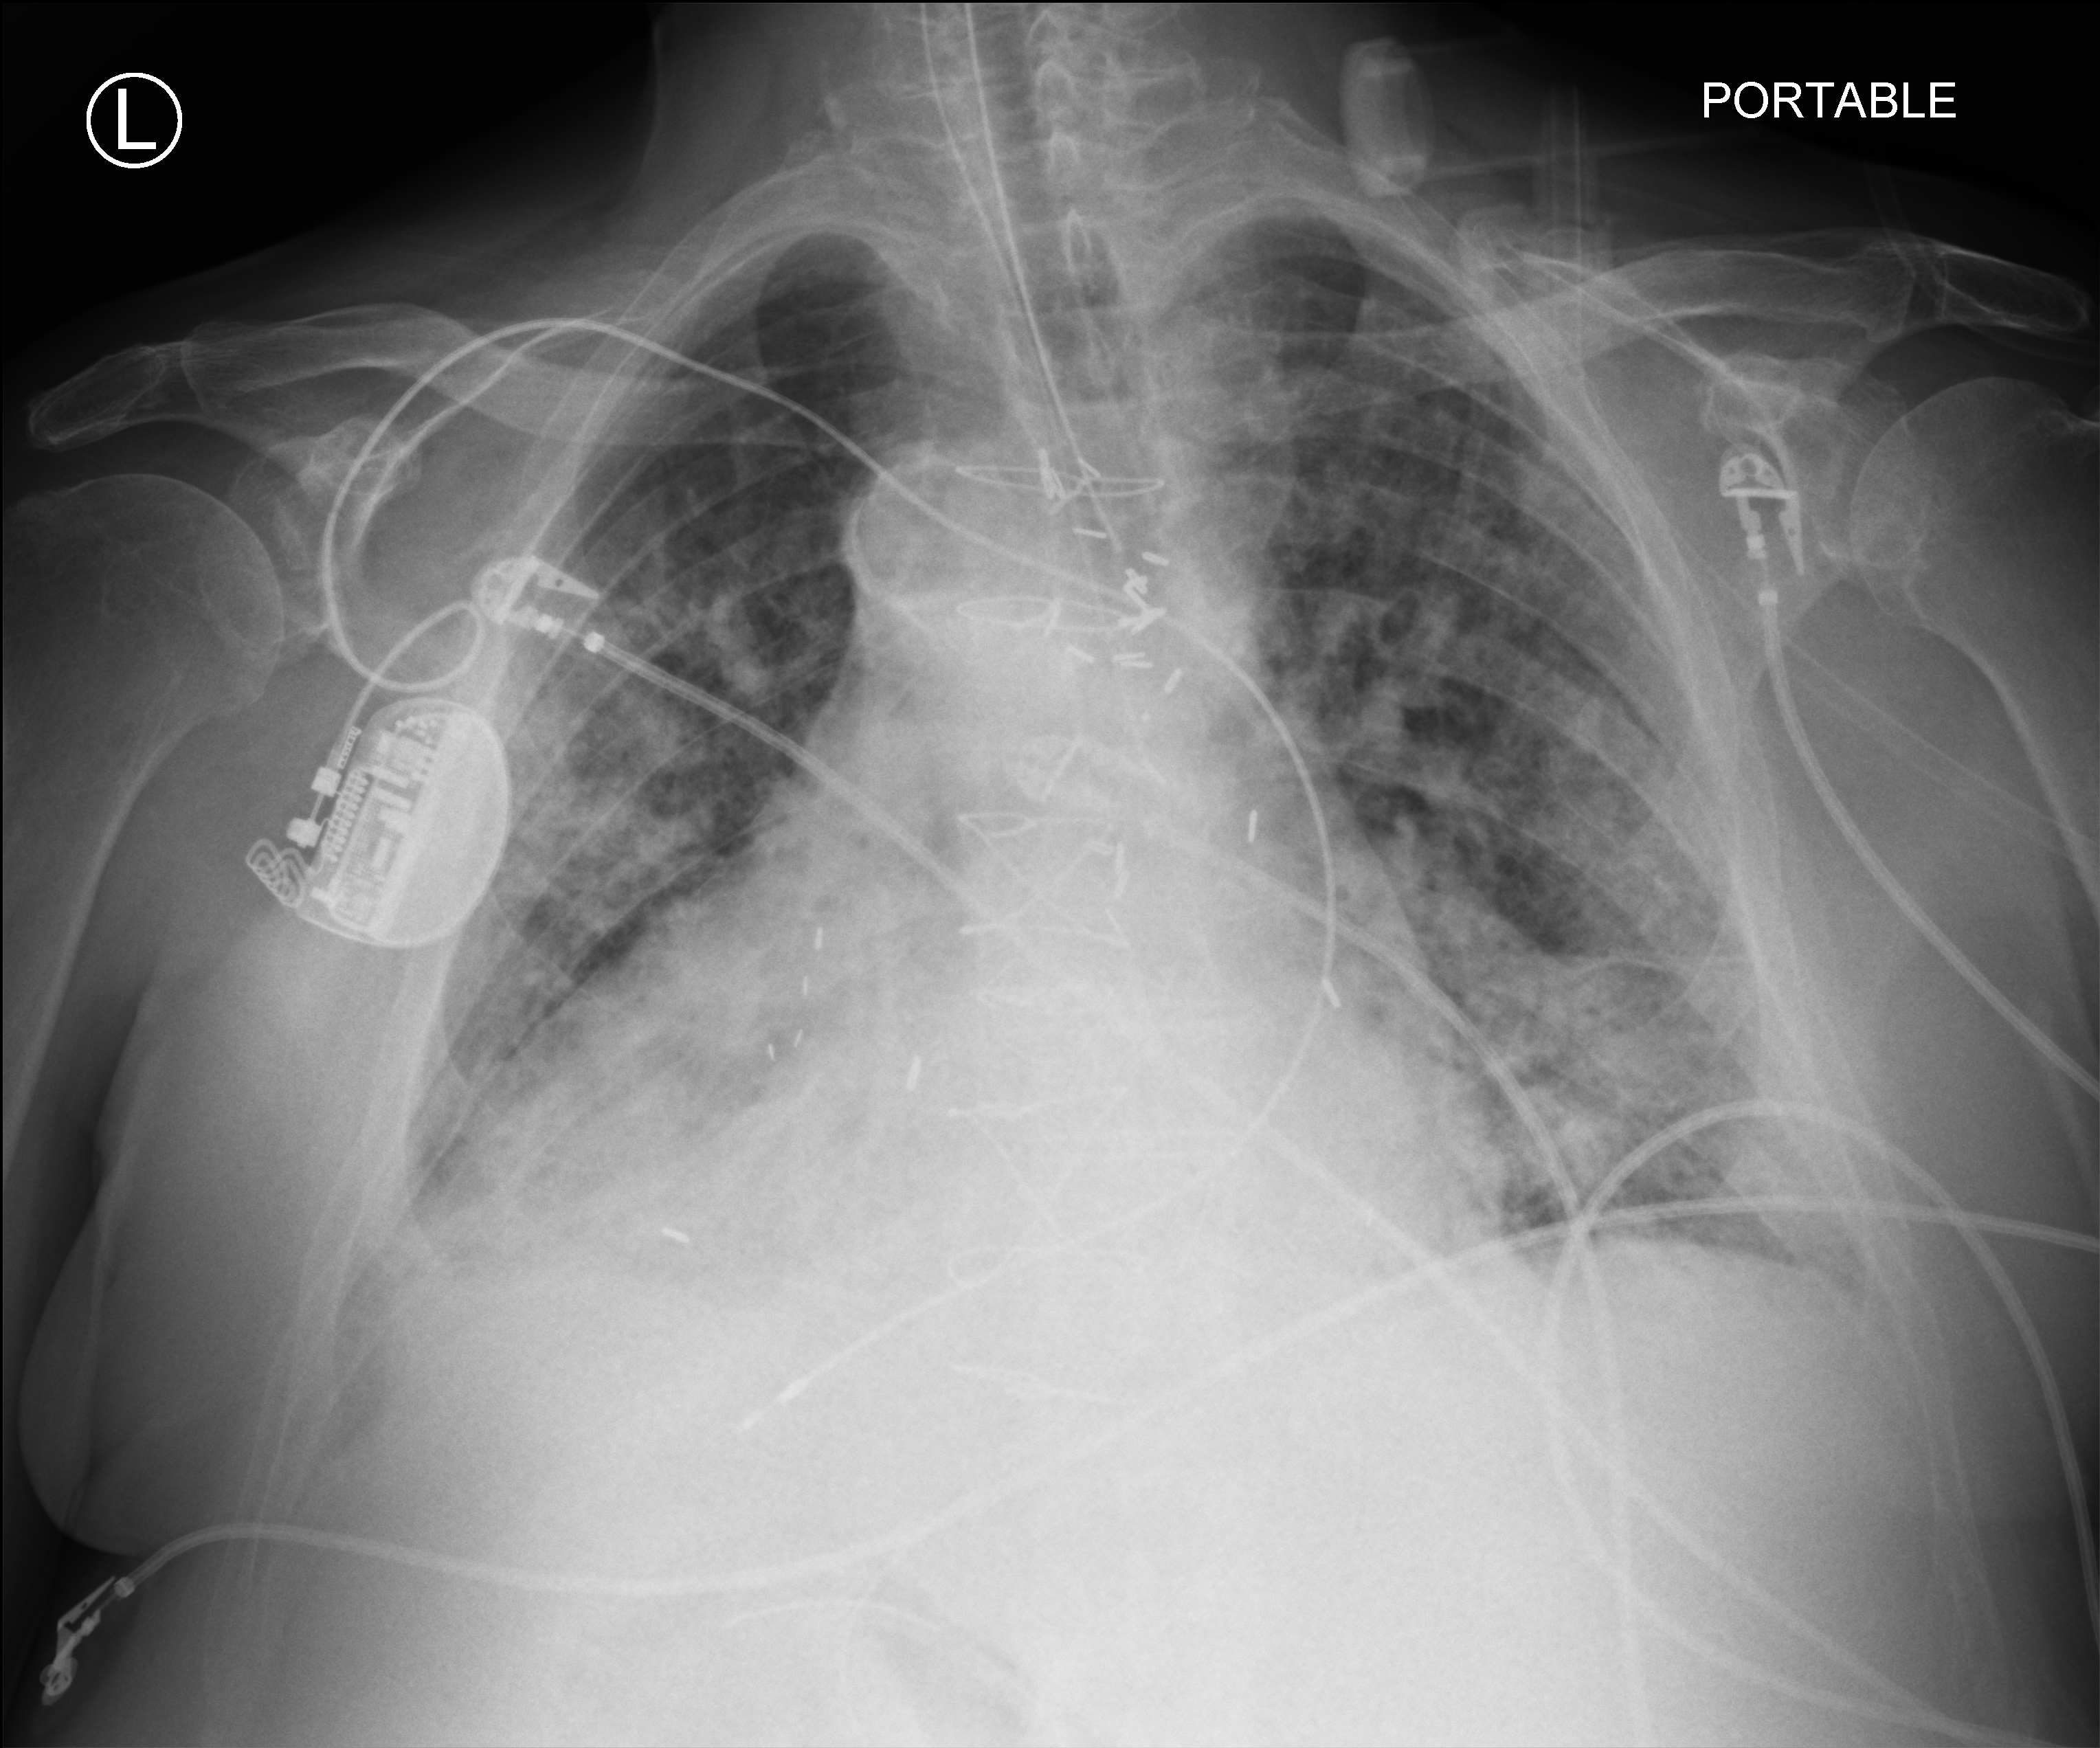
Bedside chest radiograph (computed radiography), anteroposterior (AP) projection. Male patient hospitalised with COVID-19, age 75–90 years.
Admission-level facts for this patient (not findings on this image; timing relative to this image not recorded):
- other chronic lung disease (admission record): yes
- admitted to intensive care during this hospital stay: yes
- hypertension (admission record): yes